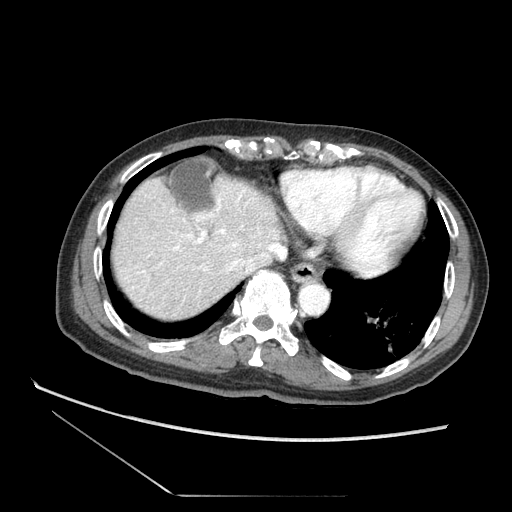
Contrast-enhanced abdominal CT (liver protocol), one axial slice. Position 65 of 73 along the scan axis. Reconstruction kernel STANDARD. 120 kVp. Soft-tissue window (W 400 / L 40 HU). 2.5 mm slice thickness. 512 × 512 image matrix. From the clinical record (not read from this slice): diagnosis: hepatocellular carcinoma (patient treated with transarterial chemoembolisation; whether this scan precedes or follows treatment is not stated here); TNM stage (as recorded): Stage-II.
Annotated regions visible in this slice (semi-automatic segmentation, software-assisted and operator-edited):
- abdominal aorta: box from (x=301, y=284) to (x=329, y=314) px
- liver parenchyma outside the tumour (the mass and vessels are separate outlines, so this box may not span the whole liver): (x=110, y=176)–(x=414, y=326)
- mass: (x=117, y=262)–(x=155, y=295)
- liver vessels: (x=162, y=214)–(x=209, y=245)